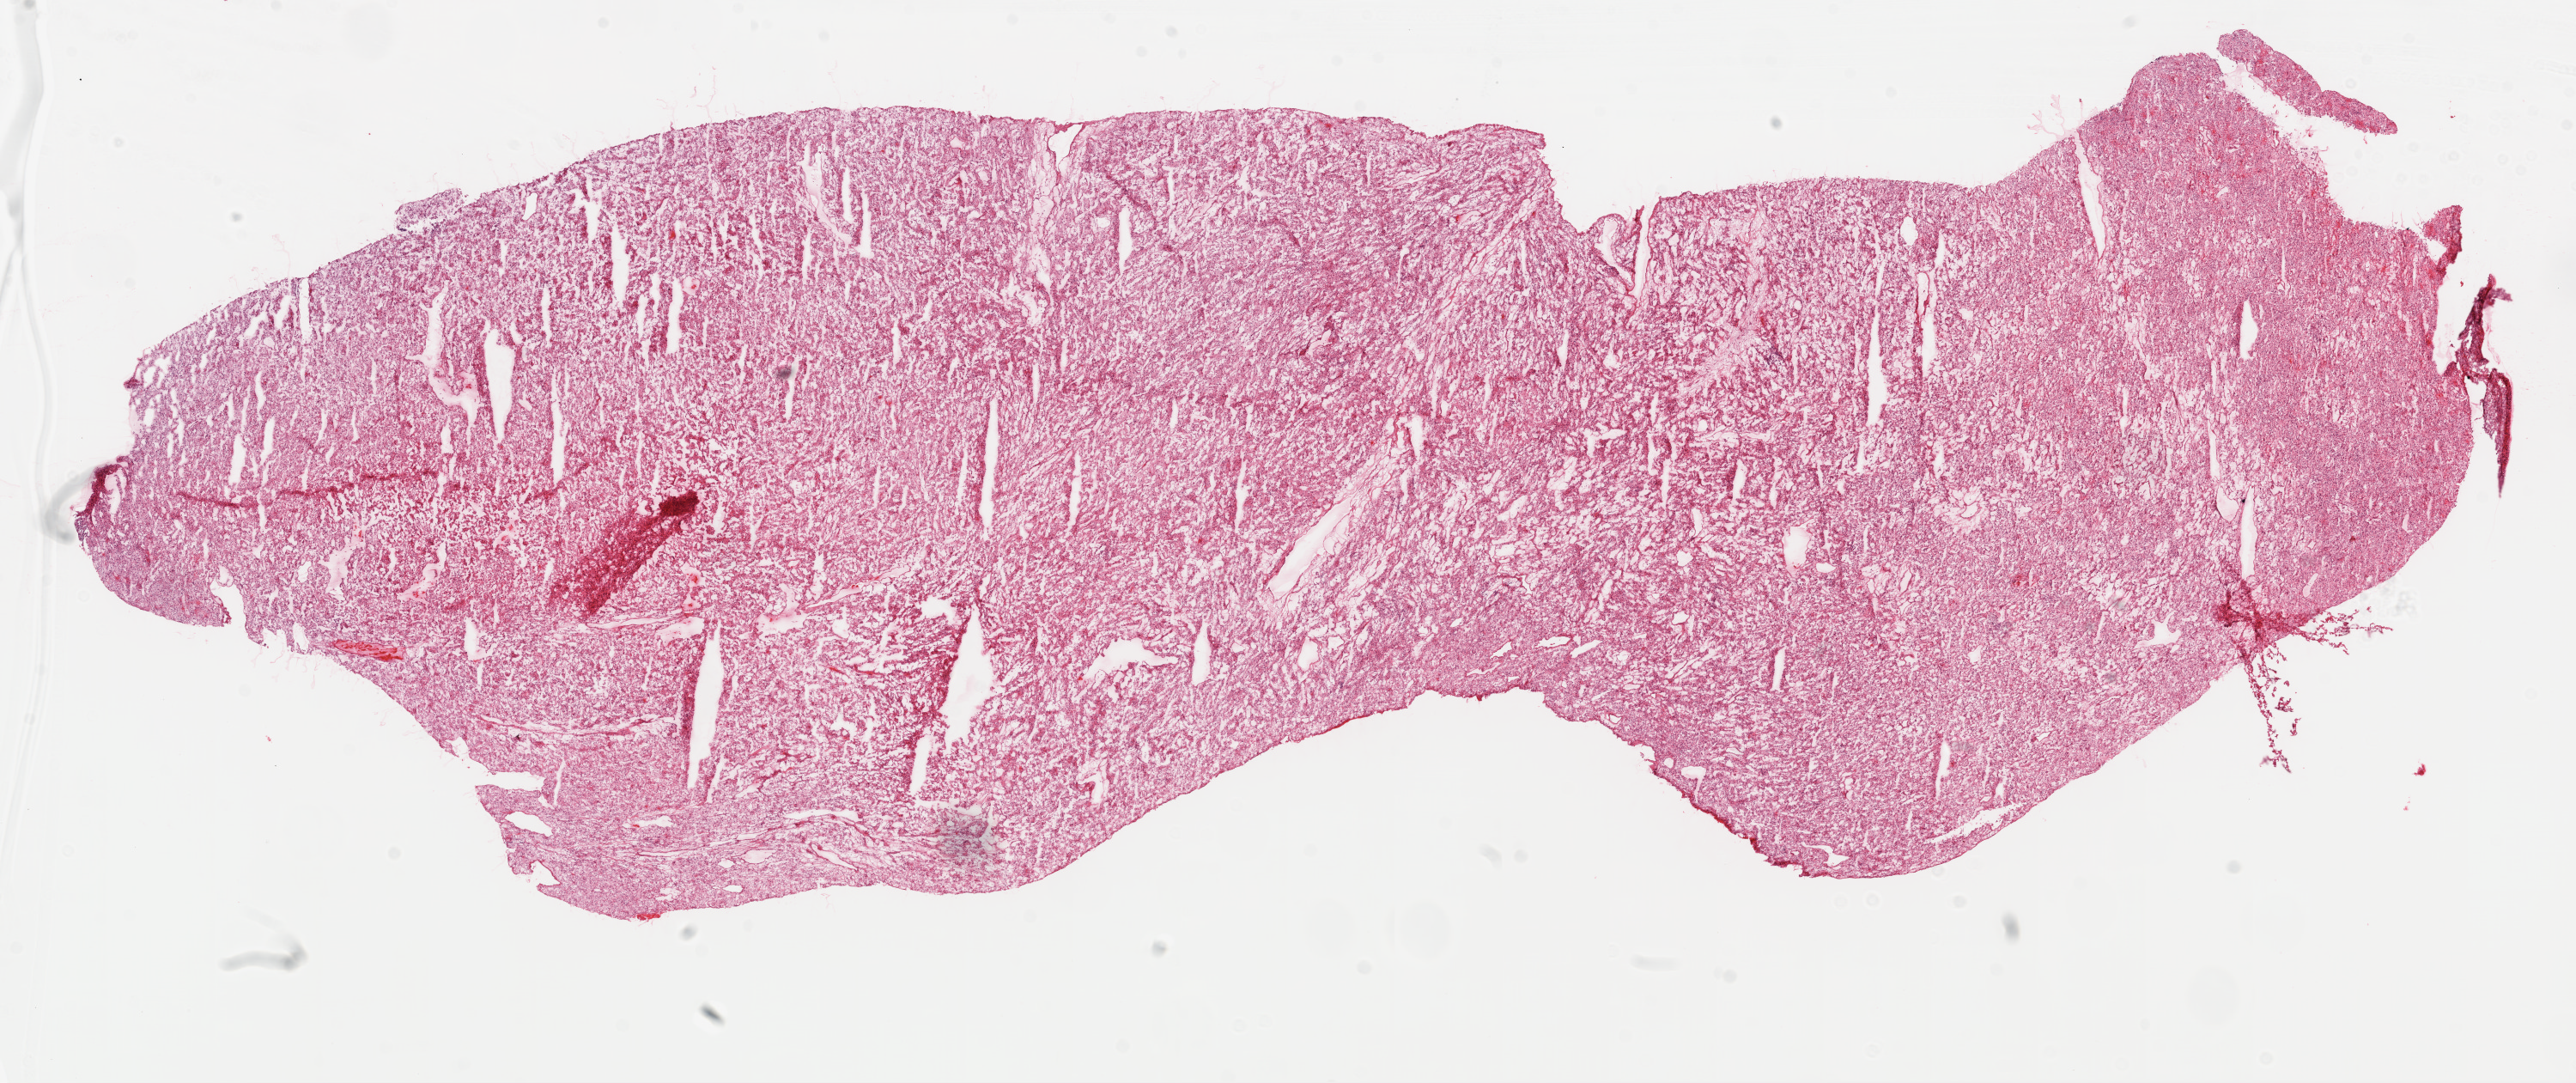
Whole-slide histology image, H&E, whole scanned area (about 24.1 x 10.1 mm, from a 20x scan) shown as a low-resolution overview; frozen section from the top of the tissue portion; sample: primary tumour, kidney. Male patient; age at initial diagnosis 43 years. Histologic grade: G3 (poorly differentiated). Slide review estimates, as recorded: tumour cells 95%, tumour nuclei 90%, normal cells 0%, stromal cells 5%, necrosis 0%. Infiltration values recorded for this section: lymphocyte infiltration 2%, monocyte infiltration 0%, neutrophil infiltration 0%.
AJCC pathologic stage: III (6th edition). Diagnosis: Clear cell adenocarcinoma, NOS. Laterality: right. TNM: T3a NX M0.